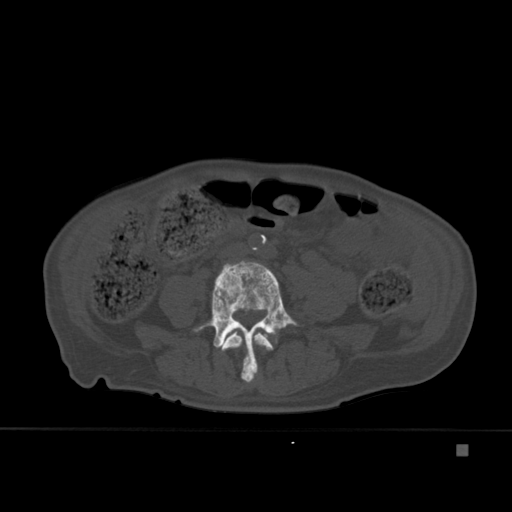
CT including the spine, one axial slice; position 127 of 451 along the scan axis; bone window (W 1800 / L 400 HU); 1.5 mm slice thickness; 512 × 512 image matrix, field of view 378 × 378 mm. Male patient, age 75 years. Case-level facts recorded for this patient, not image findings: primary cancer: prostate.
Outlined on this slice (semi-automatically segmented with operator editing):
- L3 vertebra: bounding box (x1, y1, x2, y2) in pixels: (221, 330, 274, 383)
- L4 vertebra: (194, 260, 298, 381)